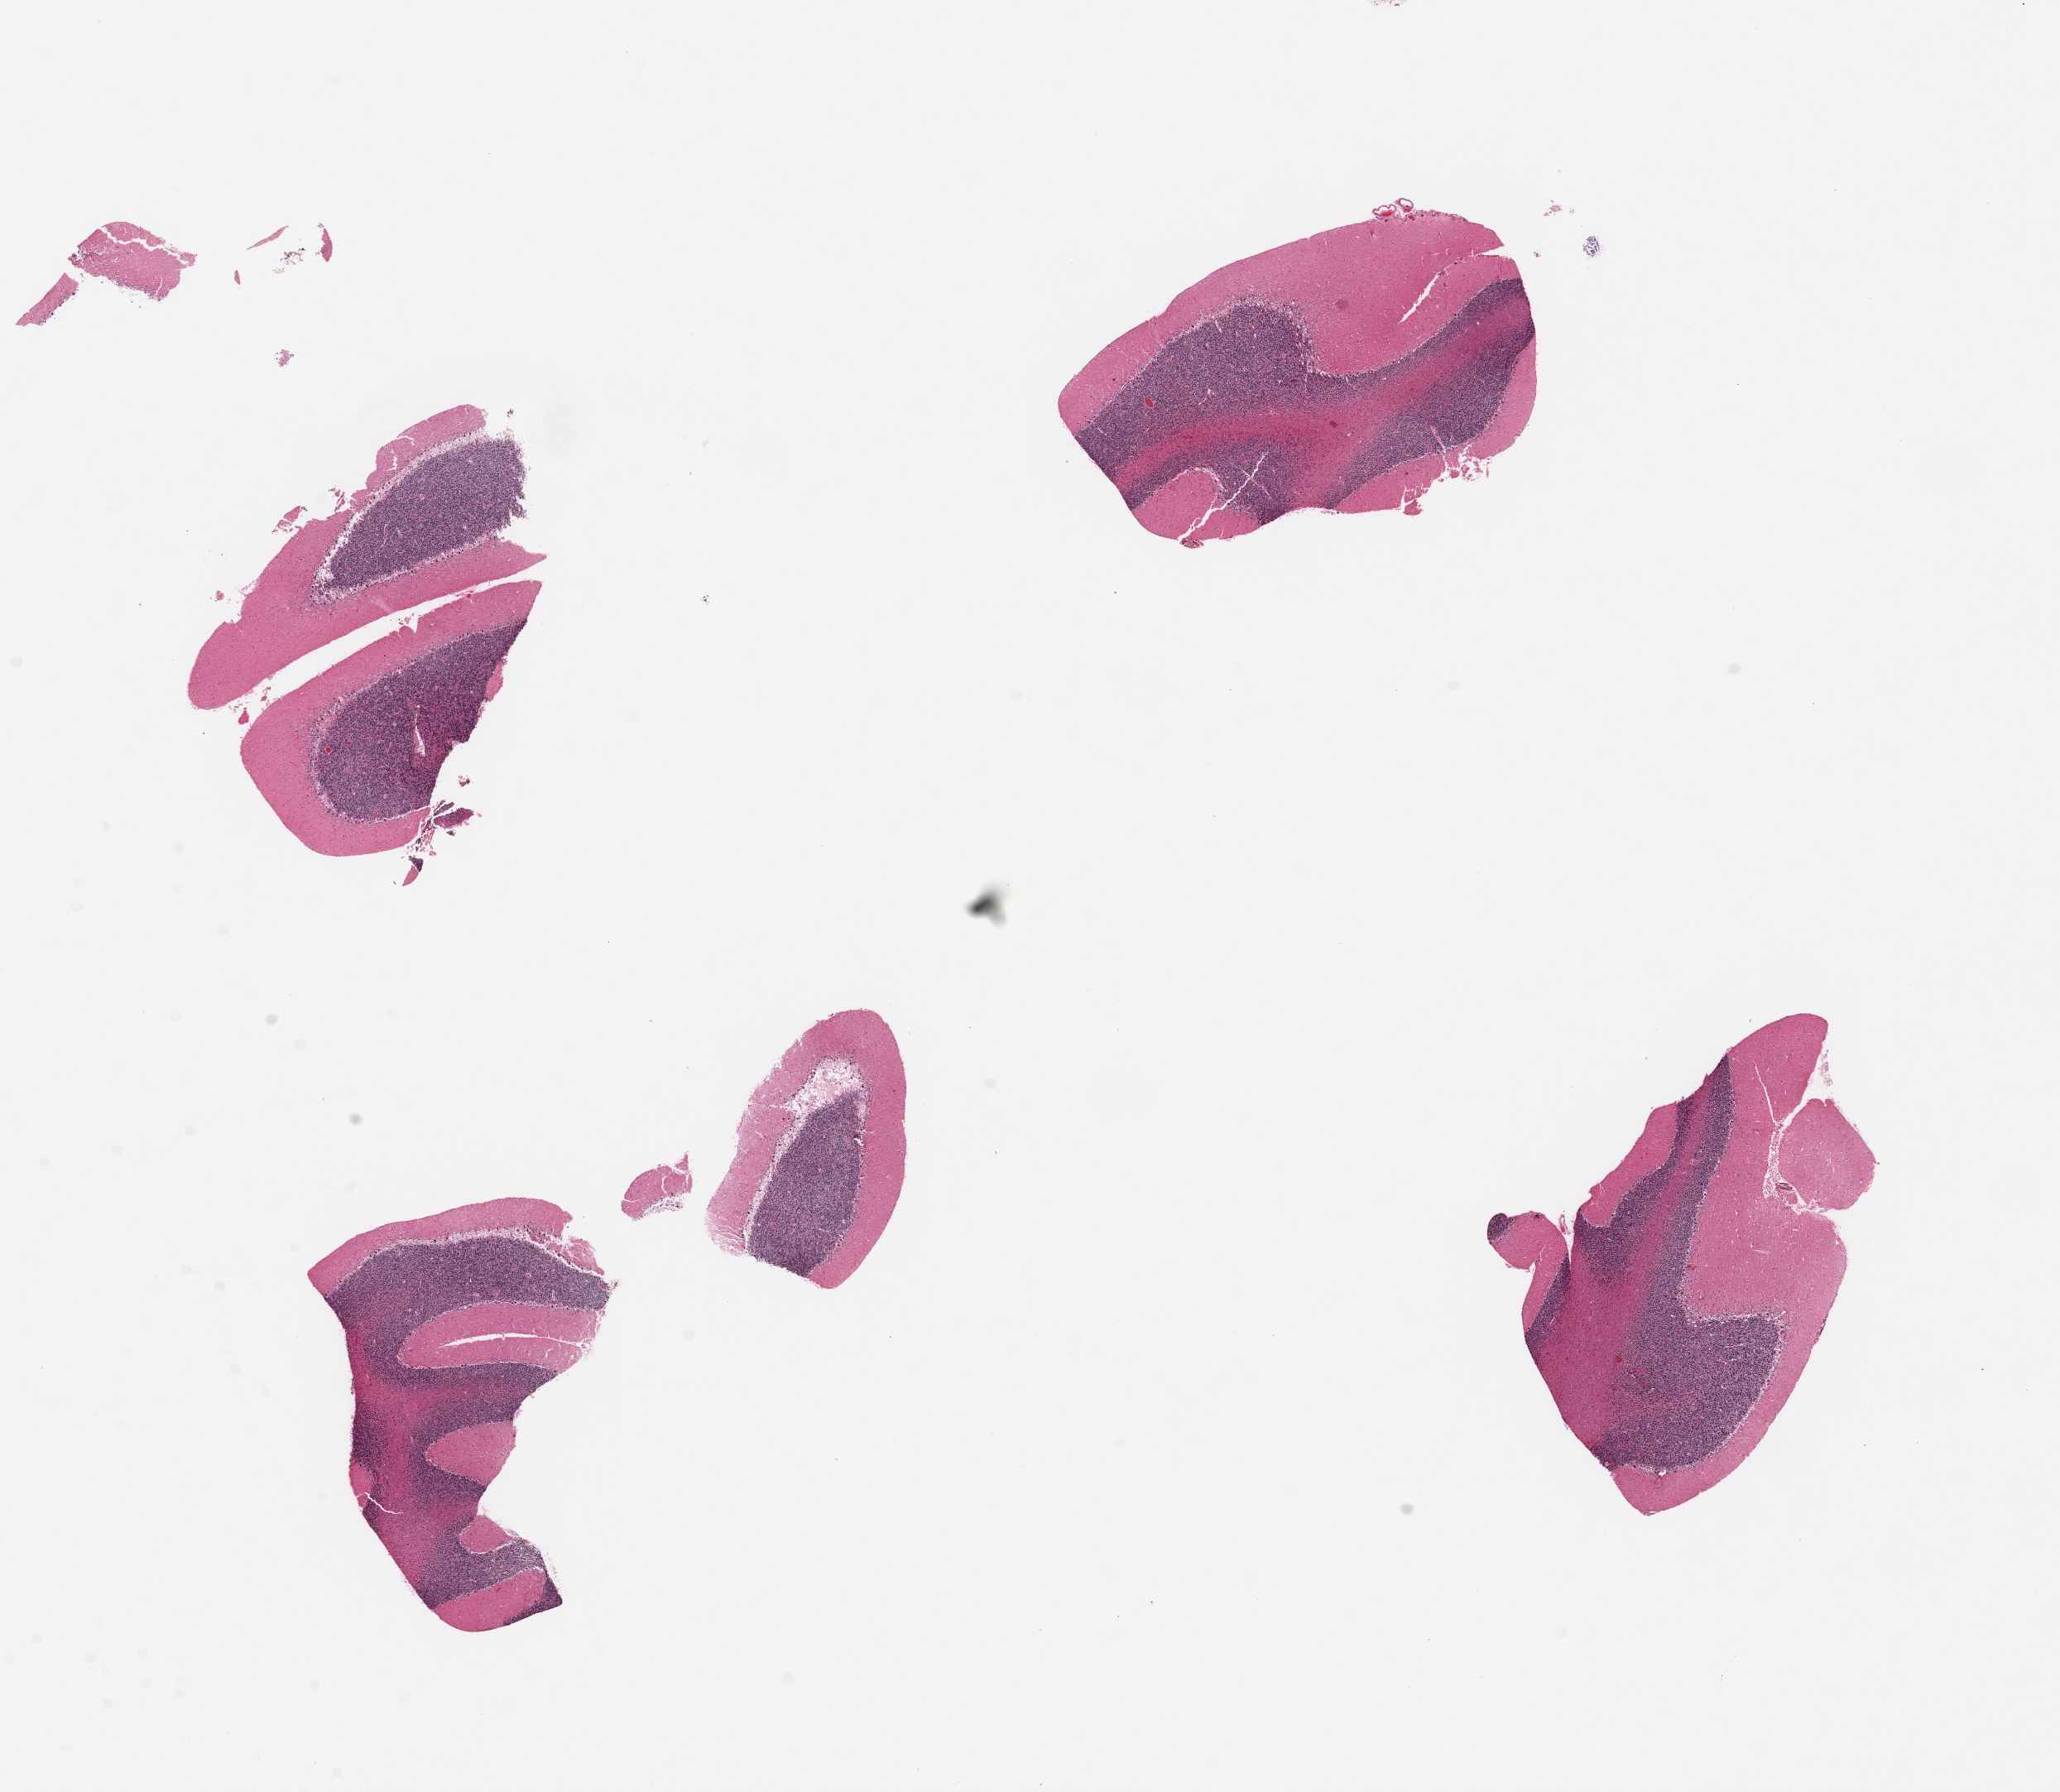
Haematoxylin and eosin whole-slide image, brightfield, shown as a low-resolution overview of the whole scanned area (about 19.7 x 17.1 mm). PAXgene-fixed, paraffin-embedded tissue. Section of cerebellum (target tissue). Tissue donor sample. Donor: male.
Review note (as recorded): 4 pieces, up to 6x4mm.